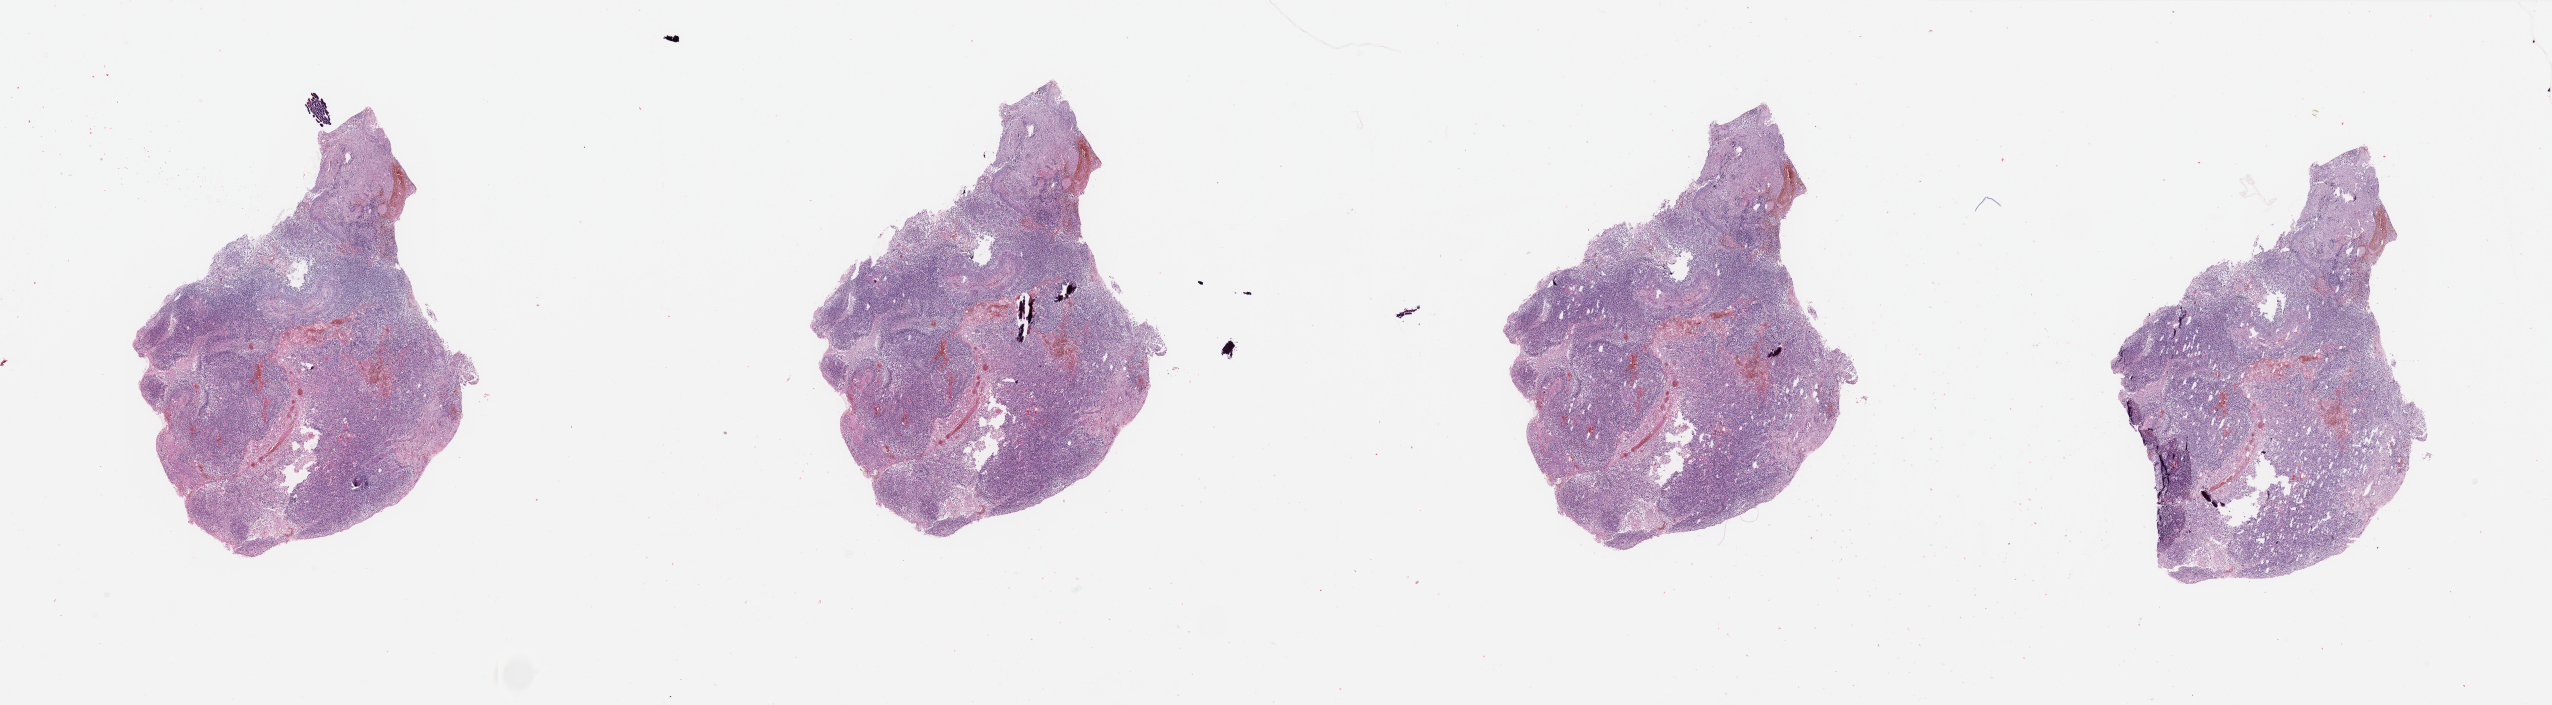
Hematoxylin and eosin (H&E) stained whole-slide image, a low-resolution overview of the entire scanned area, about 40.4 x 11.2 mm (slide scanned at 20x), brain, tumour tissue. 60-year-old female patient.
Diagnosis: Glioblastoma.